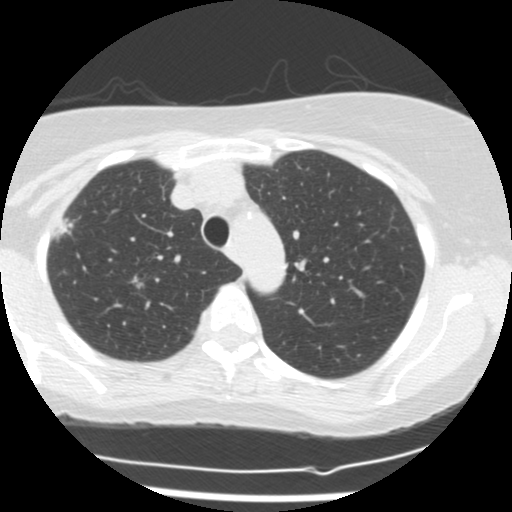
Low-dose screening chest CT, one axial slice. Position 121 of 160 along the scan axis. Reconstruction kernel STANDARD. 120 kVp. Lung window (W 1500 / L -600 HU). 2.5 mm slice thickness. 512 × 512 image matrix, field of view 300 × 300 mm.
Structures marked on this image (expert manual segmentation):
- lesion 1 (tumor, upper lobe of right lung): bounding box (x1, y1, x2, y2) in pixels: (53, 218, 75, 240)